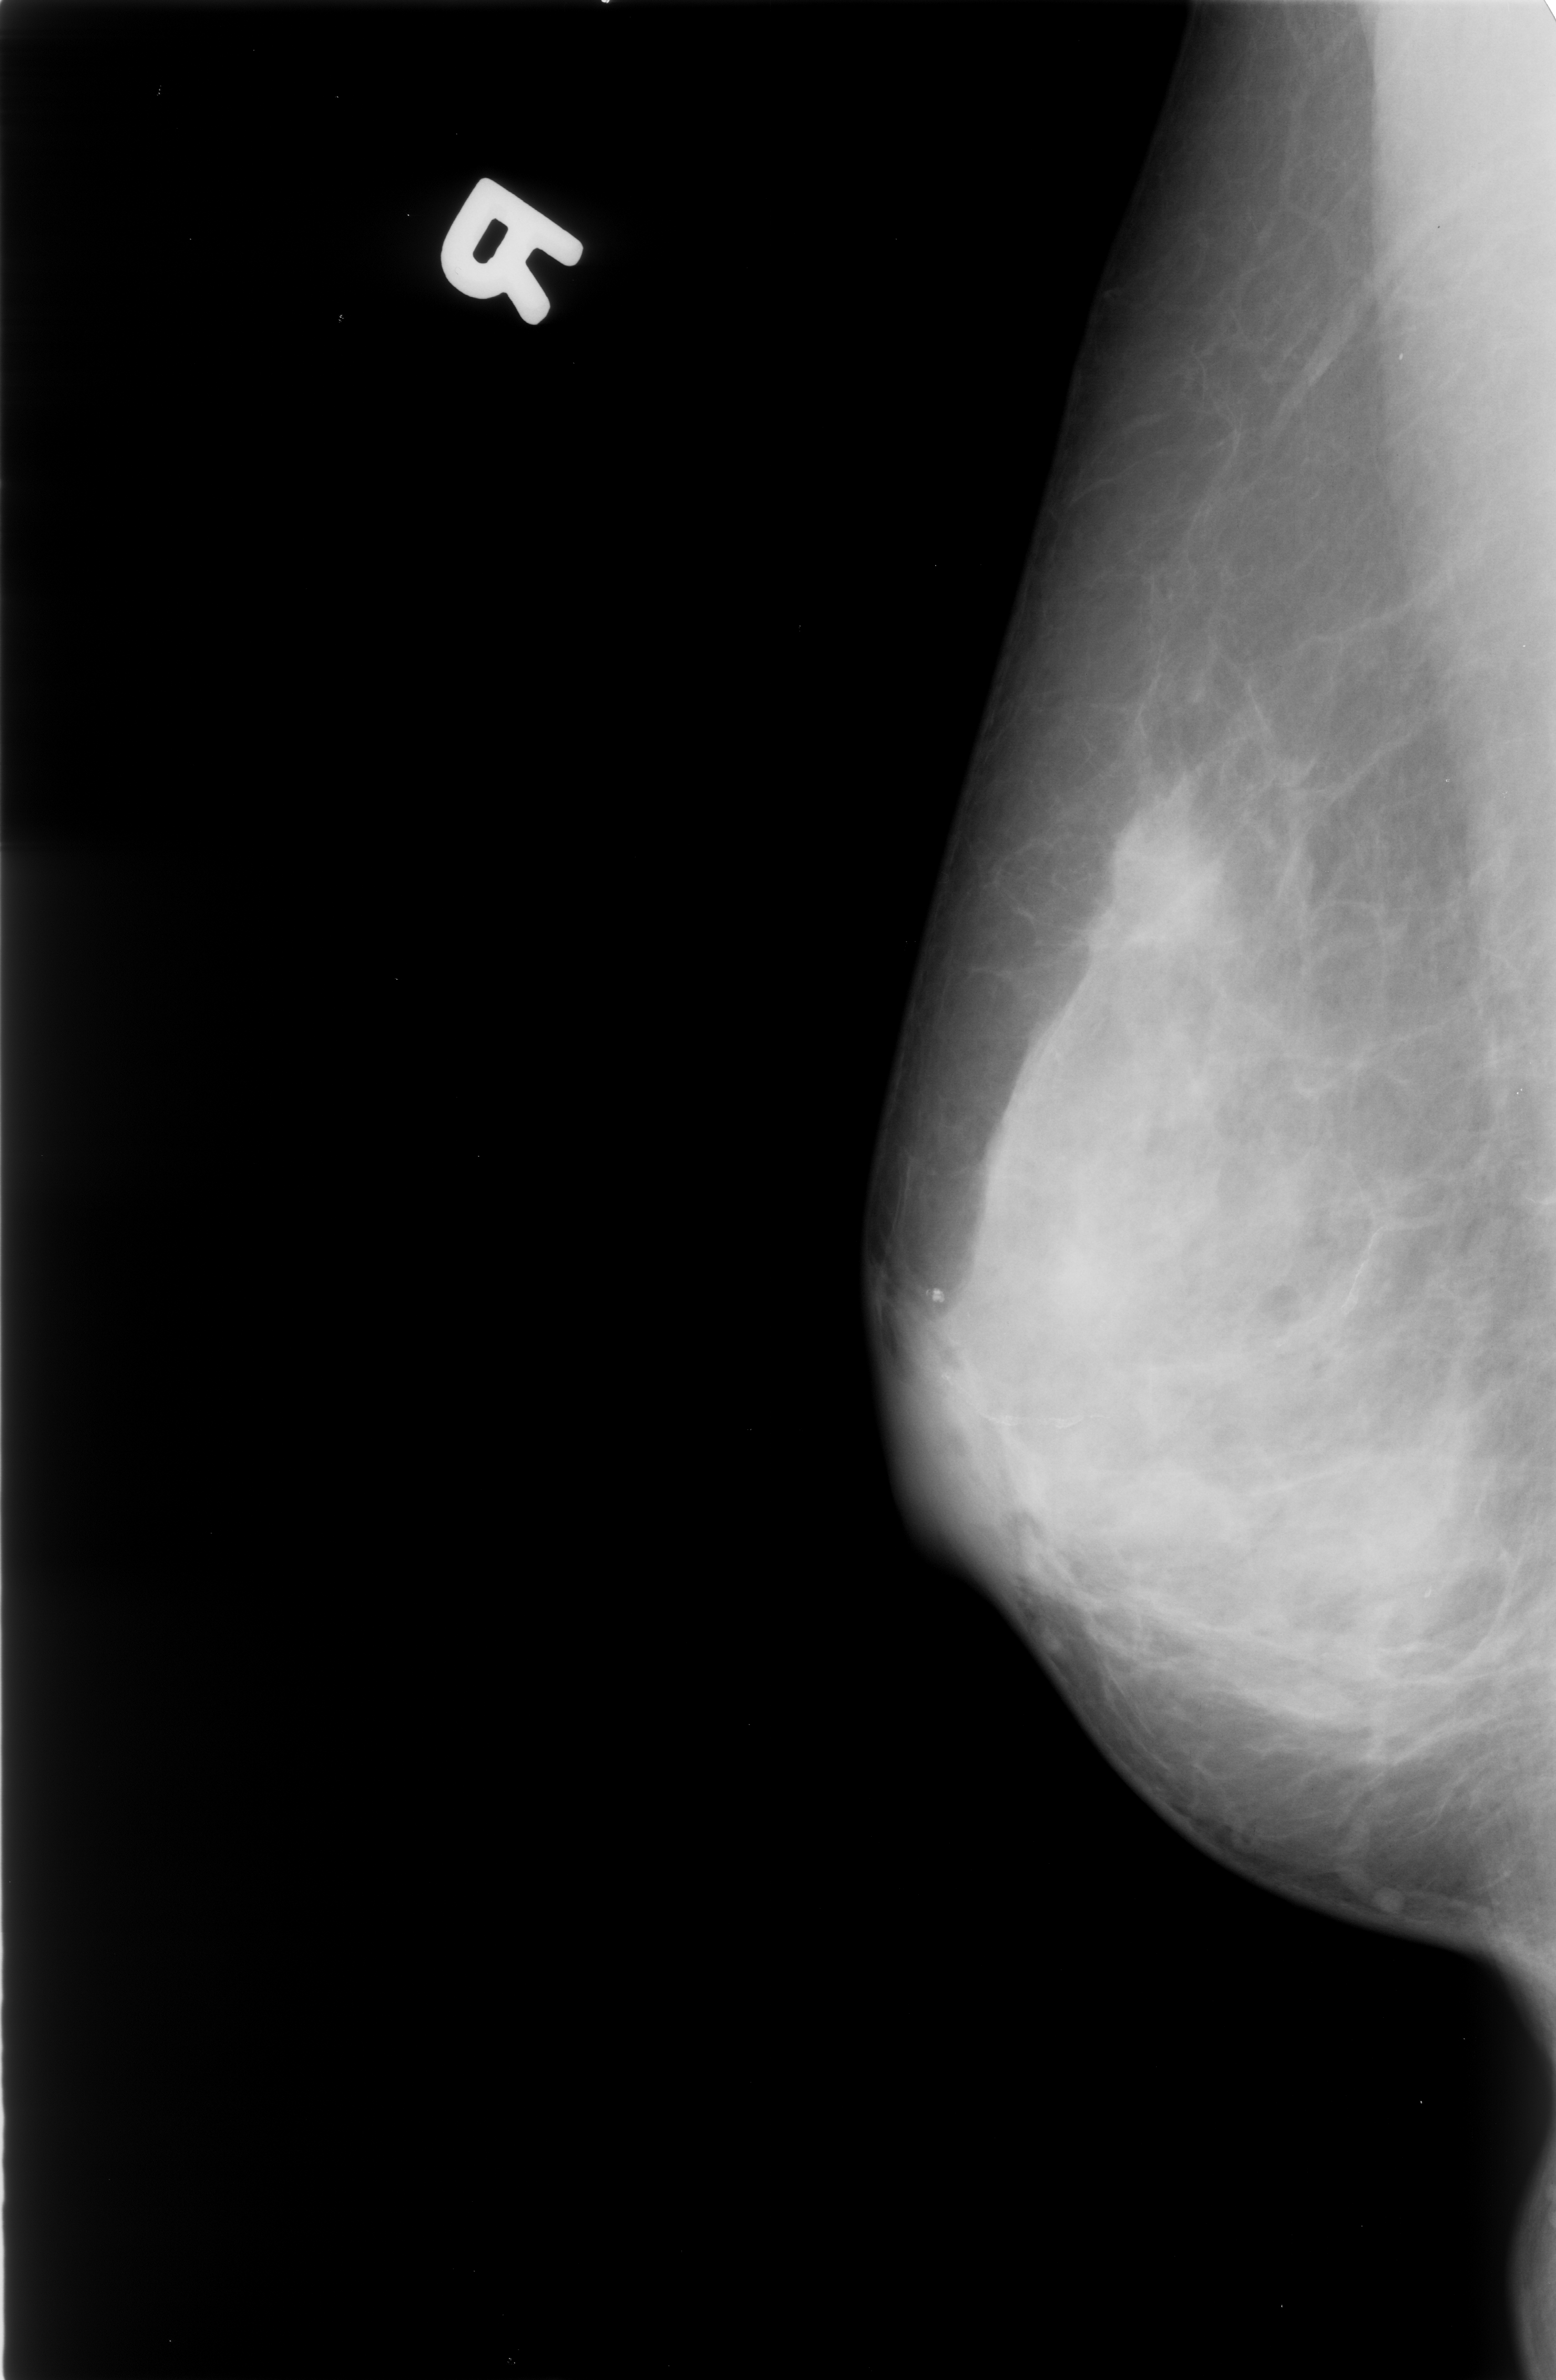
Scanned film-screen mammogram. Right breast. MLO view. Breast composition: extremely dense (BI-RADS density category 4 of 4). 1556 × 2380 image matrix.
Expert-marked regions of interest on this image (one box per marked abnormality):
- mass, shape irregular / architectural distortion, margins obscured / ill defined; BI-RADS assessment category 4; subtlety rating 3 on a 1 (subtle) to 5 (obvious) scale; pathology result (as recorded, not read from the image): malignant: bounding box (x1, y1, x2, y2) in pixels: (1075, 802, 1233, 953)